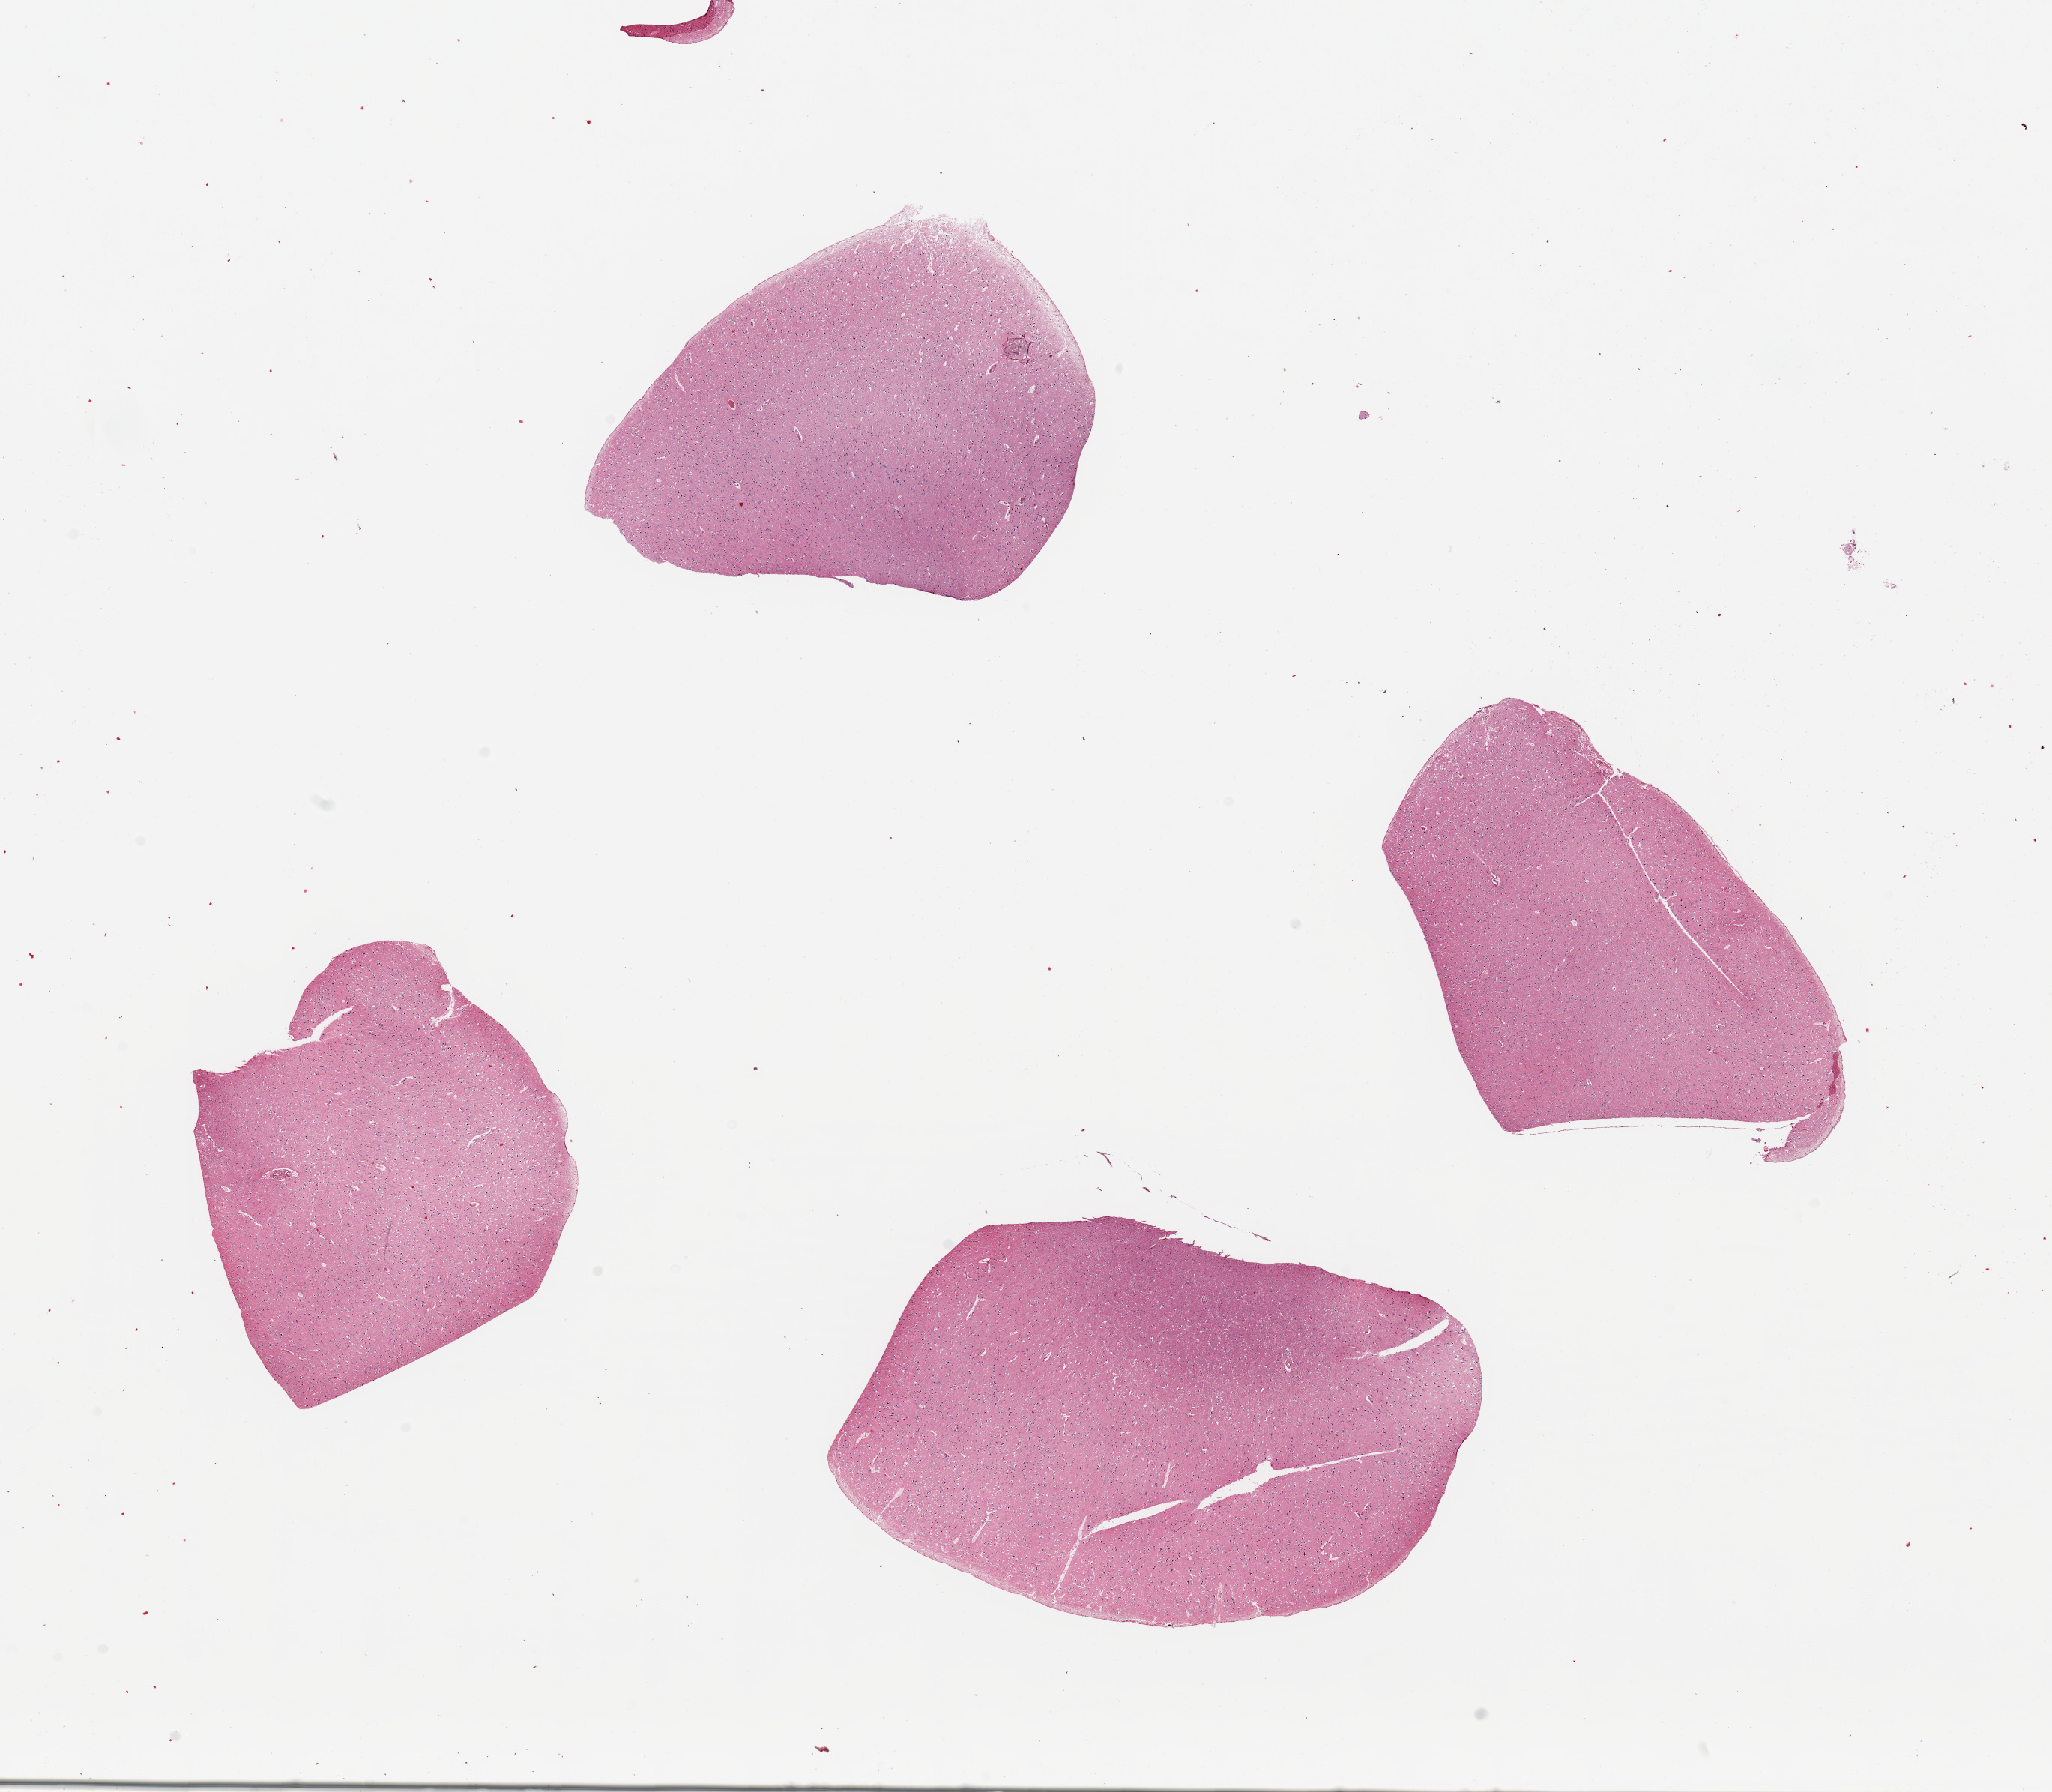
Whole-slide image, hematoxylin and eosin (H&E) stain — whole scanned area (about 21.7 x 18.9 mm, acquisition: 20x scan) shown as a low-resolution overview; PAXgene-fixed, paraffin-embedded tissue; section of cerebral cortex (target tissue); tissue donor sample. Donor: female.
• review note (as recorded): 4 pieces